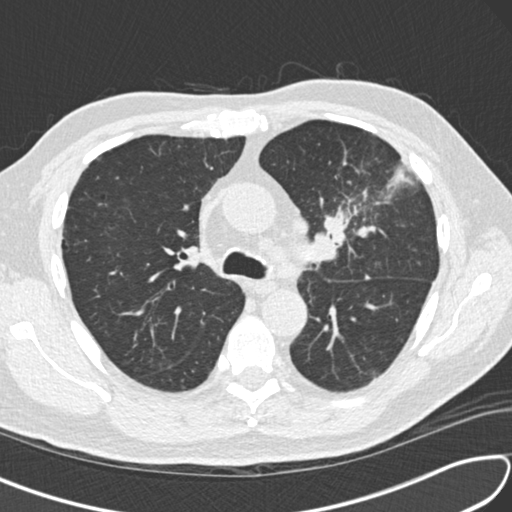
Low-dose screening chest CT, one axial slice. Slice 103 of 156 in the series (ordered by position). Reconstruction kernel B30f. 120 kVp. Lung window (W 1500 / L -600 HU). 2 mm slice thickness. 512 × 512 image matrix.
Structures marked on this image (expert manual segmentation):
- lesion 1 (tumor, upper lobe of left lung): bounding box (x1, y1, x2, y2) in pixels: (324, 212, 350, 242)